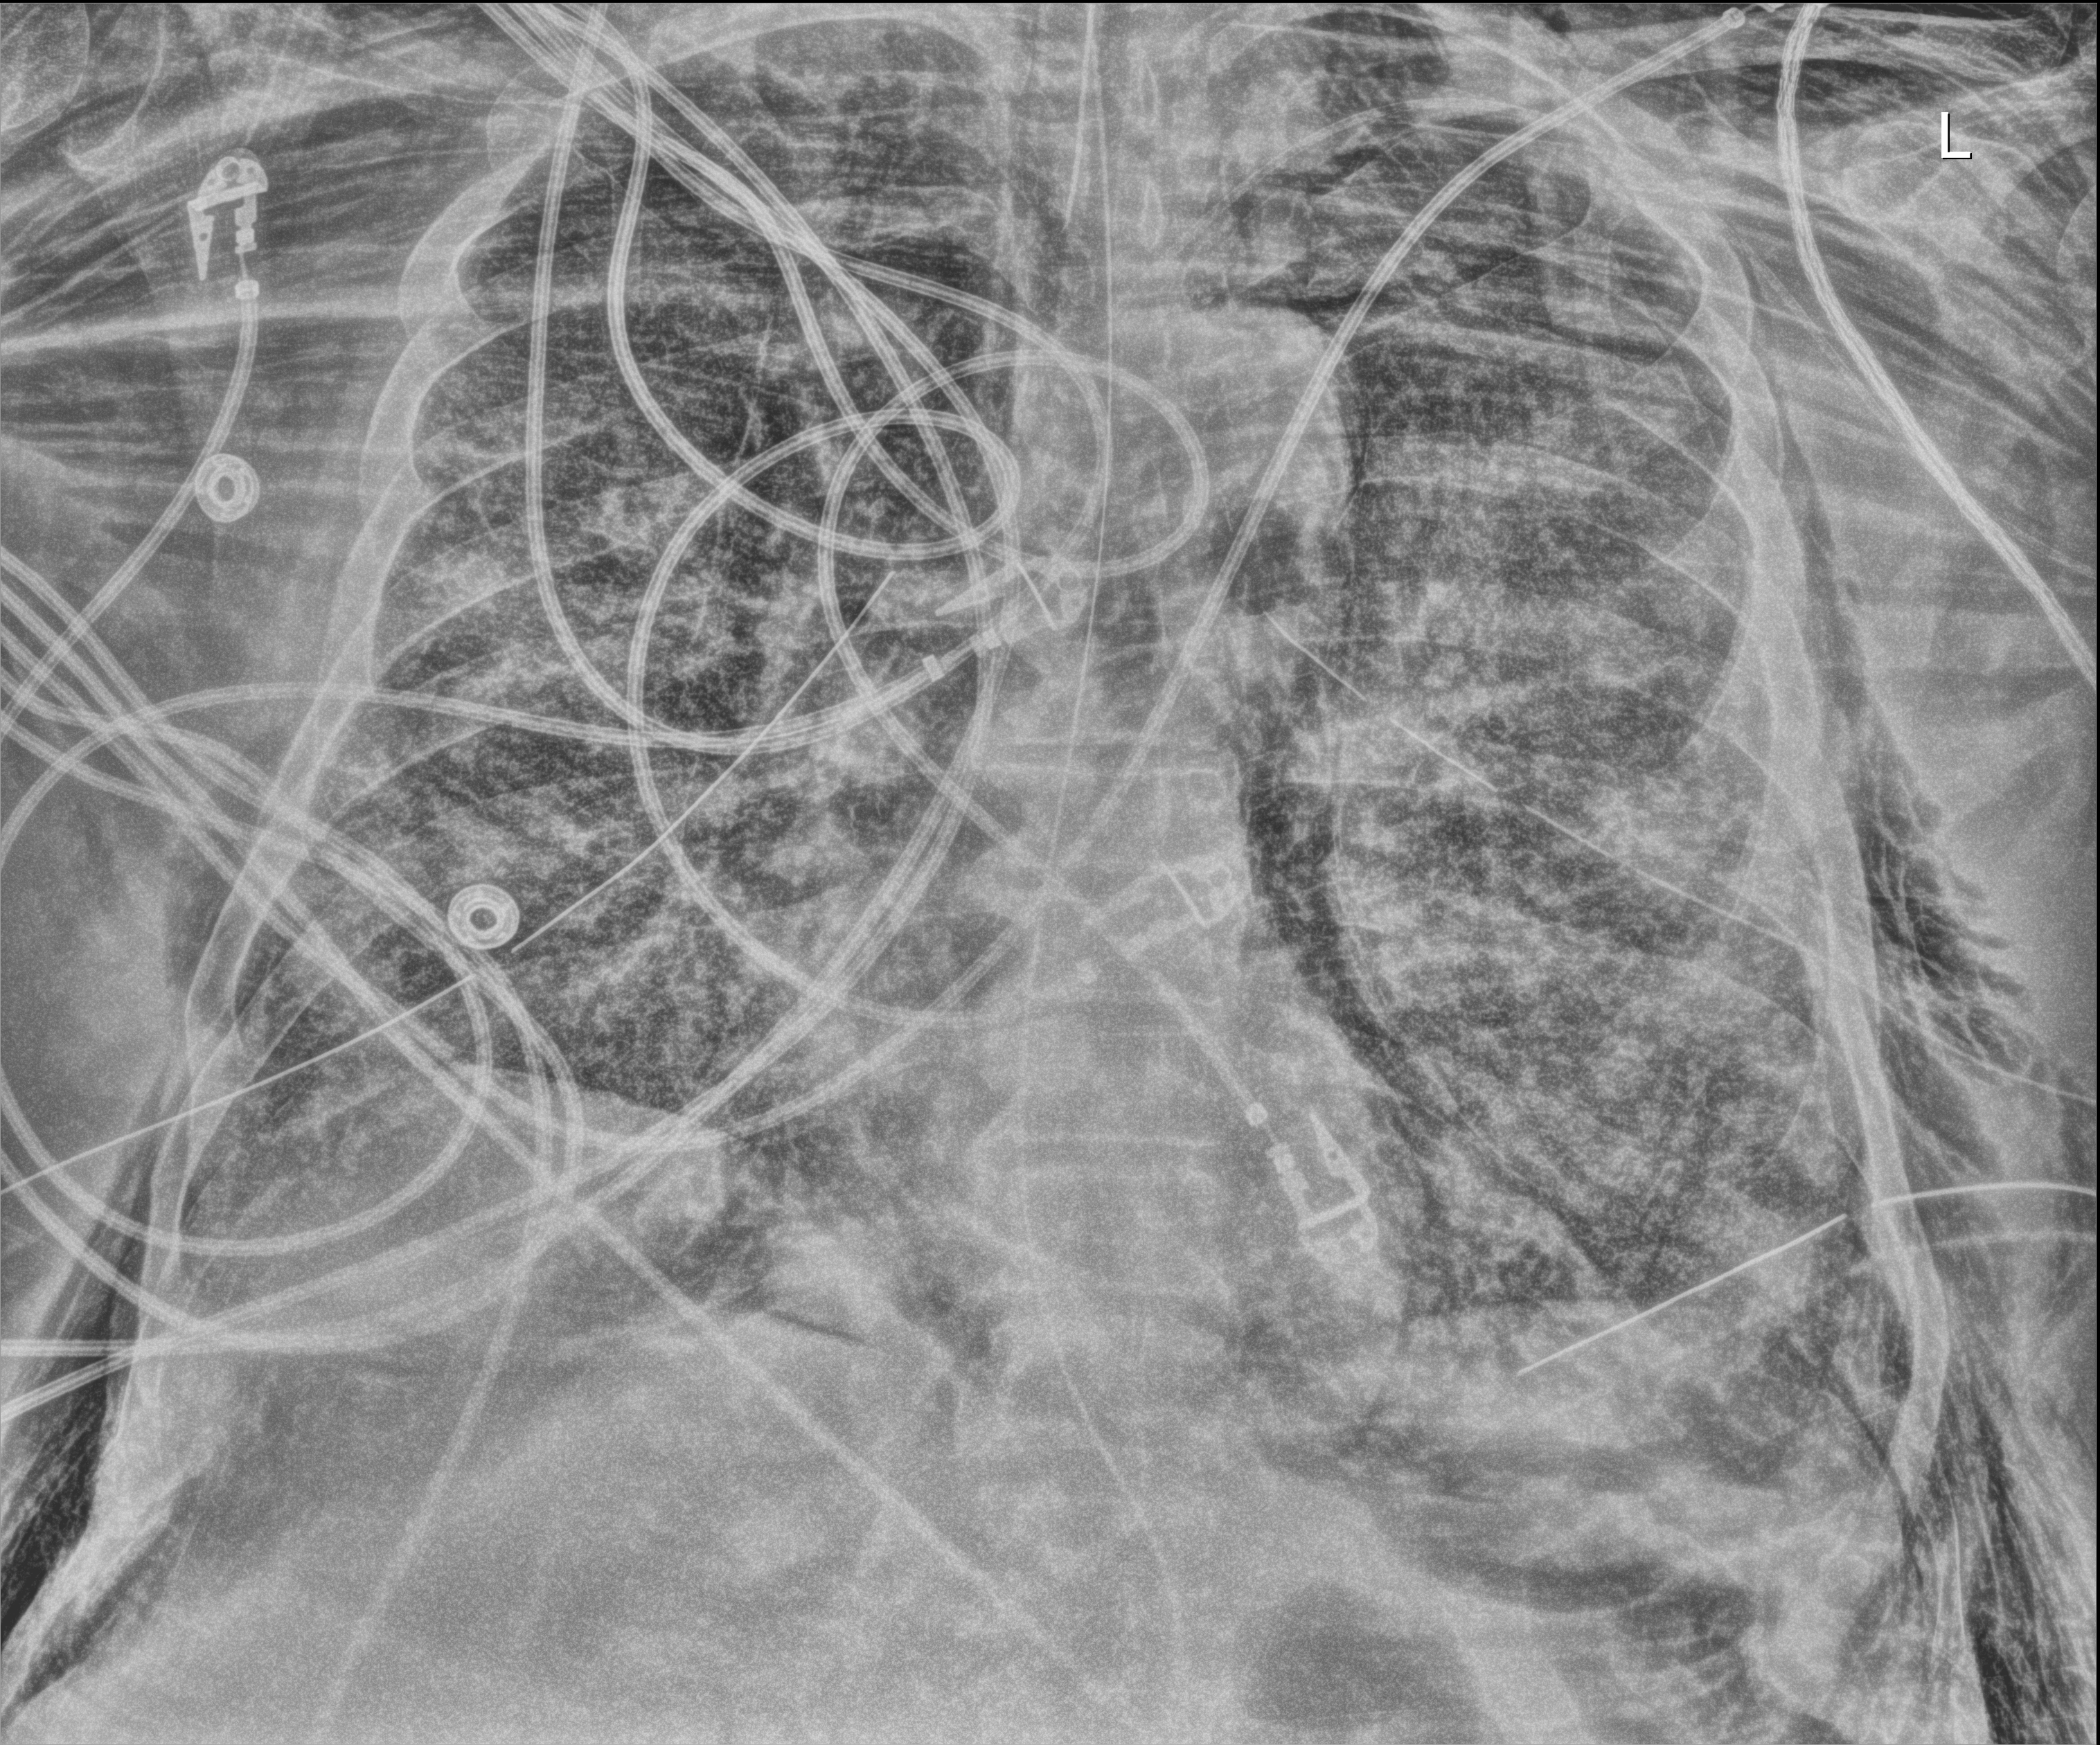
Portable chest radiograph, anteroposterior (AP) projection. Adult patient hospitalised with COVID-19, age 18–59 years.
From the hospital-stay record, not from the radiograph (when in the stay this image was taken is not recorded):
- admitted to intensive care during this hospital stay: yes
- mechanically ventilated during this hospital stay: yes
- length of hospital stay: 28 days